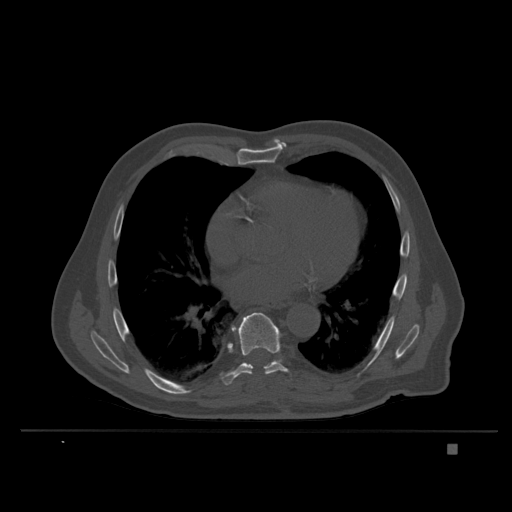
CT including the spine, one axial slice; slice 229 of 435 in the series (ordered by position); bone window (W 1800 / L 400 HU); 512 × 512 image matrix, field of view 434 × 434 mm. Patient: male, 73 years. Case-level facts recorded for this patient, not image findings: primary cancer: skin.
Structures marked on this image (semi-automatically segmented with operator editing):
- T7 vertebra: bounding box <232,328,234,331> (left, top, right, bottom; pixels)
- T8 vertebra: <221,312,288,385>
- T9 vertebra: <271,361,274,364>